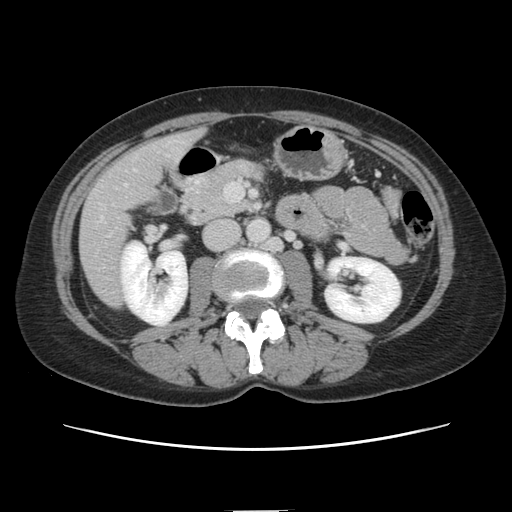
Contrast-enhanced abdominal CT, one axial slice. Position 45 of 141 along the scan axis. 120 kVp. Soft-tissue window (W 400 / L 40 HU). 512 × 512 image matrix, field of view 350 × 350 mm. Female patient, age 63 years. Case-level facts recorded for this patient, not image findings: diagnosis: colorectal cancer liver metastases, imaged before liver resection; multiple liver metastases: yes; largest metastasis: 3.2 cm; disease in both lobes: yes.
Structures marked on this image (expert manual segmentation):
- liver: bounding box <81,131,201,308> (left, top, right, bottom; pixels)
- planned liver remnant (the part of the liver to remain after resection): <182,131,201,153>
- portal vein (with intrahepatic branches): <100,217,103,220>